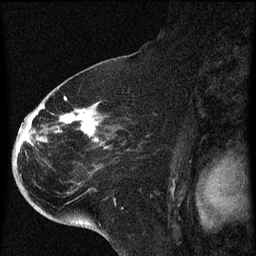
Breast MRI (dynamic contrast-enhanced), one sagittal slice; position 37 of 60 along the scan axis; dynamic contrast-enhanced series, image 2 of 4 at this slice position (ordered by acquisition); 1.5 T; TE 4.2 ms, TR 8 ms; 2 mm slice thickness; 256 × 256 image matrix, field of view 180 × 180 mm. Female patient, age 71 years.
Outlined on this slice (semi-automatically segmented with operator editing):
- analysis volume of interest (the breast-tissue region the enhancement analysis was run in; not a lesion): bounding box <32,86,141,205> (left, top, right, bottom; pixels)
- tumour enhancement mask (voxels above the 70 % enhancement threshold inside the analysis volume of interest): <39,96,98,143>